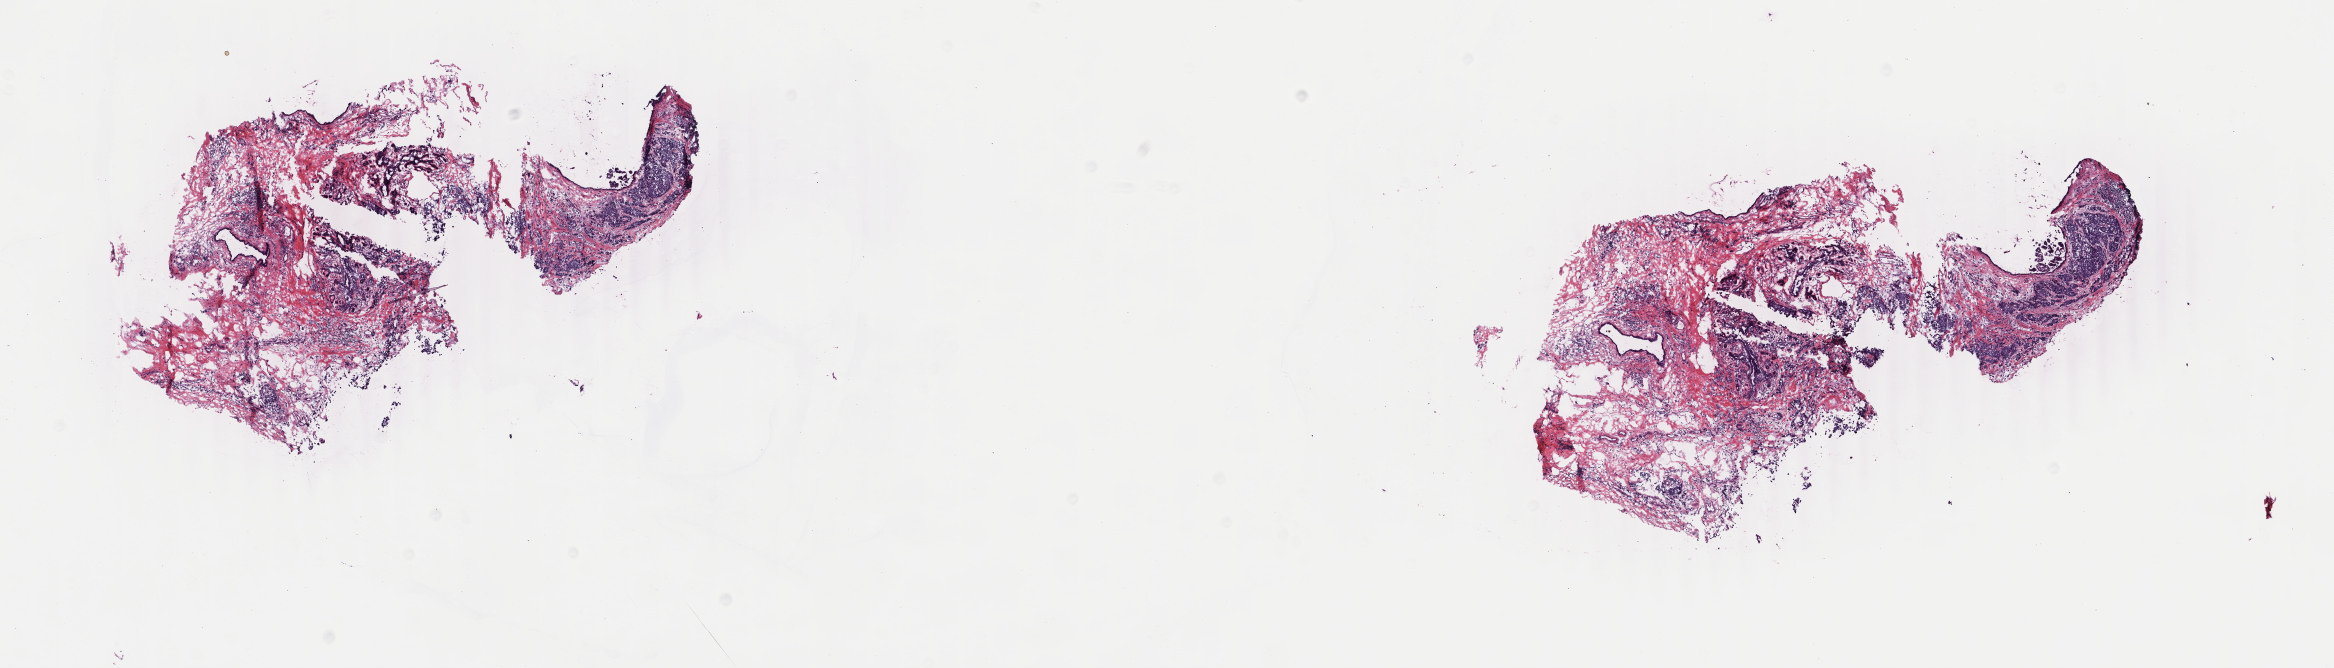
Whole-slide histology image, Hematoxylin and eosin (H&E) stained, whole scanned area (about 18.6 x 5.3 mm) shown as a low-resolution overview; frozen section from the bottom of the tissue portion; breast, primary tumour sample. Female, age 71 years at initial diagnosis. Pathologist review of this section (percent, as recorded): tumour cells 65%, tumour nuclei 65%, normal cells 3%, stromal cells 32%, necrosis 0%. Infiltration values recorded for this section: lymphocyte infiltration 5%, monocyte infiltration 0%, neutrophil infiltration 0%.
• laterality: left
• pathologic diagnosis: Infiltrating duct mixed with other types of carcinoma
• AJCC pathologic stage: IIB